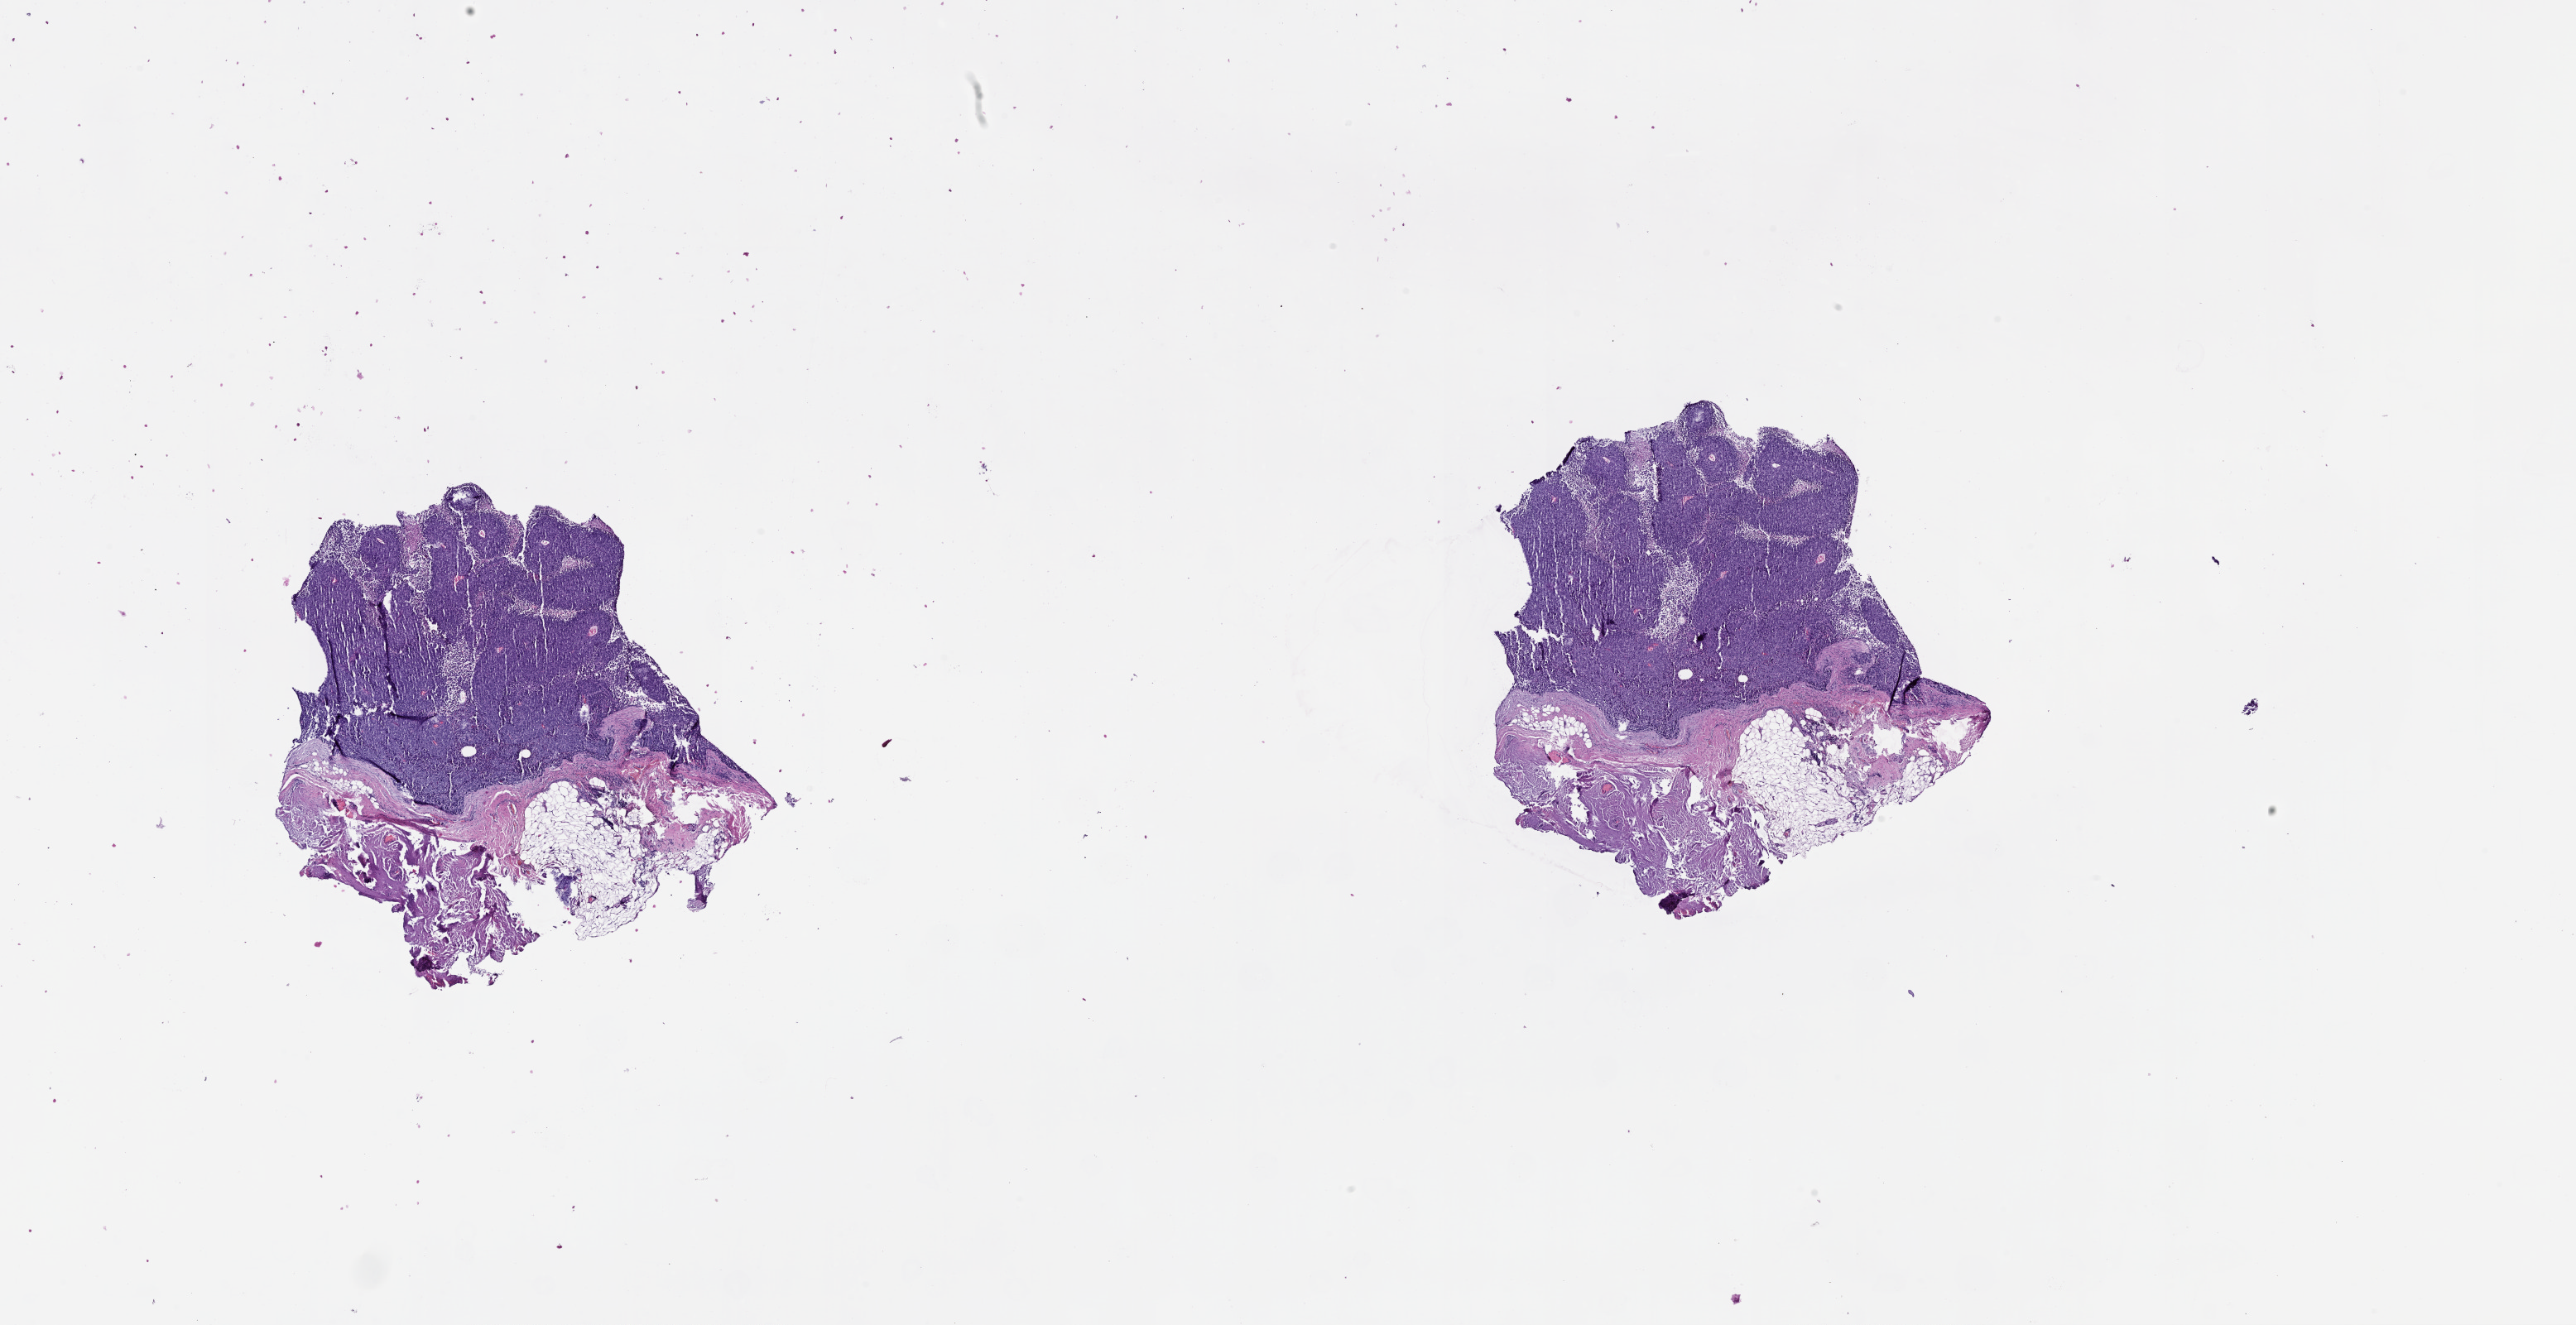
Digitized H&E tissue section (whole slide), low-resolution overview of the scanned area, about 25.1 x 12.9 mm. Male, 53 y/o.
* patient diagnosis: Malignant melanoma, NOS